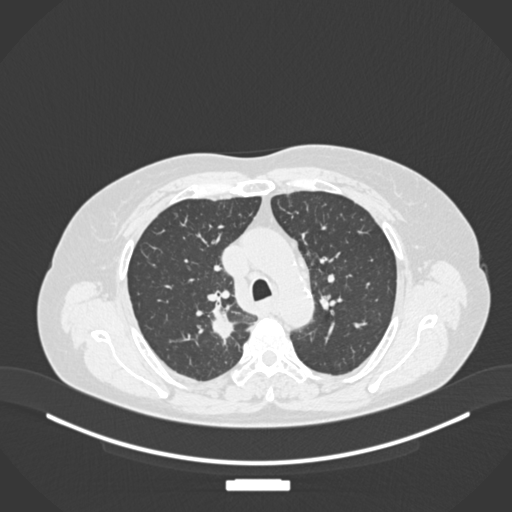
Chest CT, one axial slice. Position 181 of 237 along the scan axis. Reconstruction kernel B30f. Lung window (W 1500 / L -600 HU). 1 mm slice thickness. 512 × 512 image matrix, field of view 400 × 400 mm. Patient: female, 62 years. Case-level facts recorded for this patient, not image findings: clinical TNM (as recorded): T1c N1 M0.
Outlined on this slice (rectangle marked by the reading radiologist):
- lung tumour (recorded histology: squamous cell carcinoma): box from (x=206, y=296) to (x=237, y=345) px